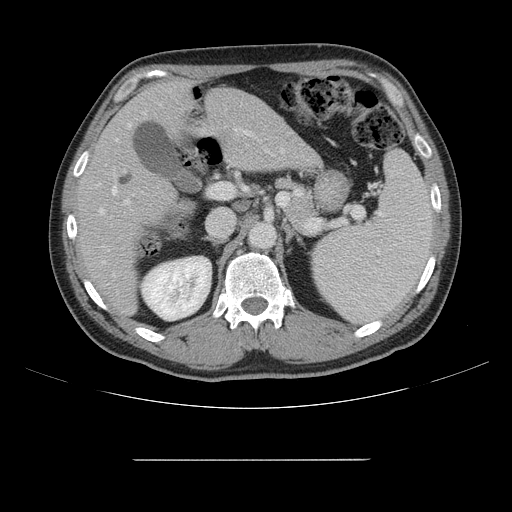
Contrast-enhanced abdominal CT, one axial slice; slice 90 of 164 in the series (ordered by position); 120 kVp; intravenous contrast given; soft-tissue window (W 400 / L 40 HU); 2.5 mm slice thickness; 512 × 512 image matrix, field of view 404 × 404 mm. Male patient, age 54 years. Case-level facts recorded for this patient, not image findings: diagnosis: colorectal cancer liver metastases, imaged before liver resection; multiple liver metastases: yes; largest metastasis: 1 cm; chemotherapy before resection: yes.
Structures marked on this image (manually delineated by an expert):
- hepatic veins: box from (x=99, y=148) to (x=284, y=263) px
- liver: (x=79, y=81)–(x=317, y=314)
- planned liver remnant (the part of the liver to remain after resection): (x=80, y=81)–(x=231, y=314)
- portal vein (with intrahepatic branches): (x=117, y=112)–(x=253, y=204)